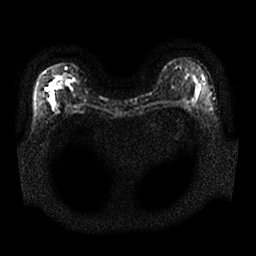
Breast MRI, one axial slice; slice 16 of 25 in the series (ordered by position); diffusion-weighted series; image 2 of 4 stored at this slice position (different b-values; order by instance number); 1.5 T; 4 mm slice thickness; 256 × 256 image matrix, field of view 340 × 340 mm. Female patient.
Structures marked on this image (manually delineated by an expert):
- tumour on diffusion-weighted imaging: bounding box [x1, y1, x2, y2] px = [50, 75, 63, 110]